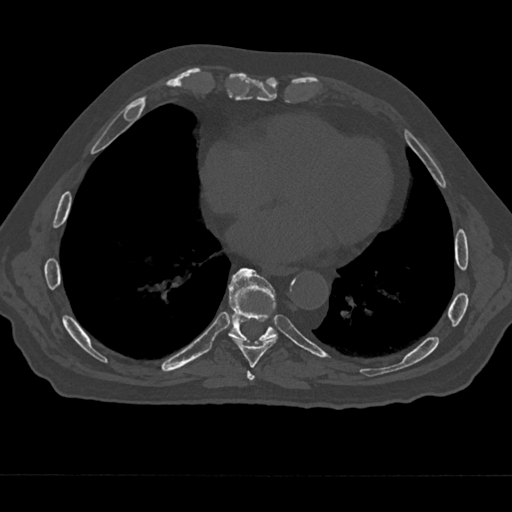
CT including the spine, one axial slice; slice 292 of 797 in the series (ordered by position); 120 kVp; bone window (W 1800 / L 400 HU); 512 × 512 image matrix, field of view 377 × 377 mm. Patient: male, 75 years. From the clinical record (not read from this slice): primary cancer: renal; vertebrae with lytic lesions (as recorded): T4.
Annotated regions visible in this slice (semi-automatically segmented with operator editing):
- T7 vertebra: bounding box (x1, y1, x2, y2) in pixels: (246, 371, 255, 385)
- T8 vertebra: (232, 290, 278, 368)
- T9 vertebra: (228, 268, 277, 342)